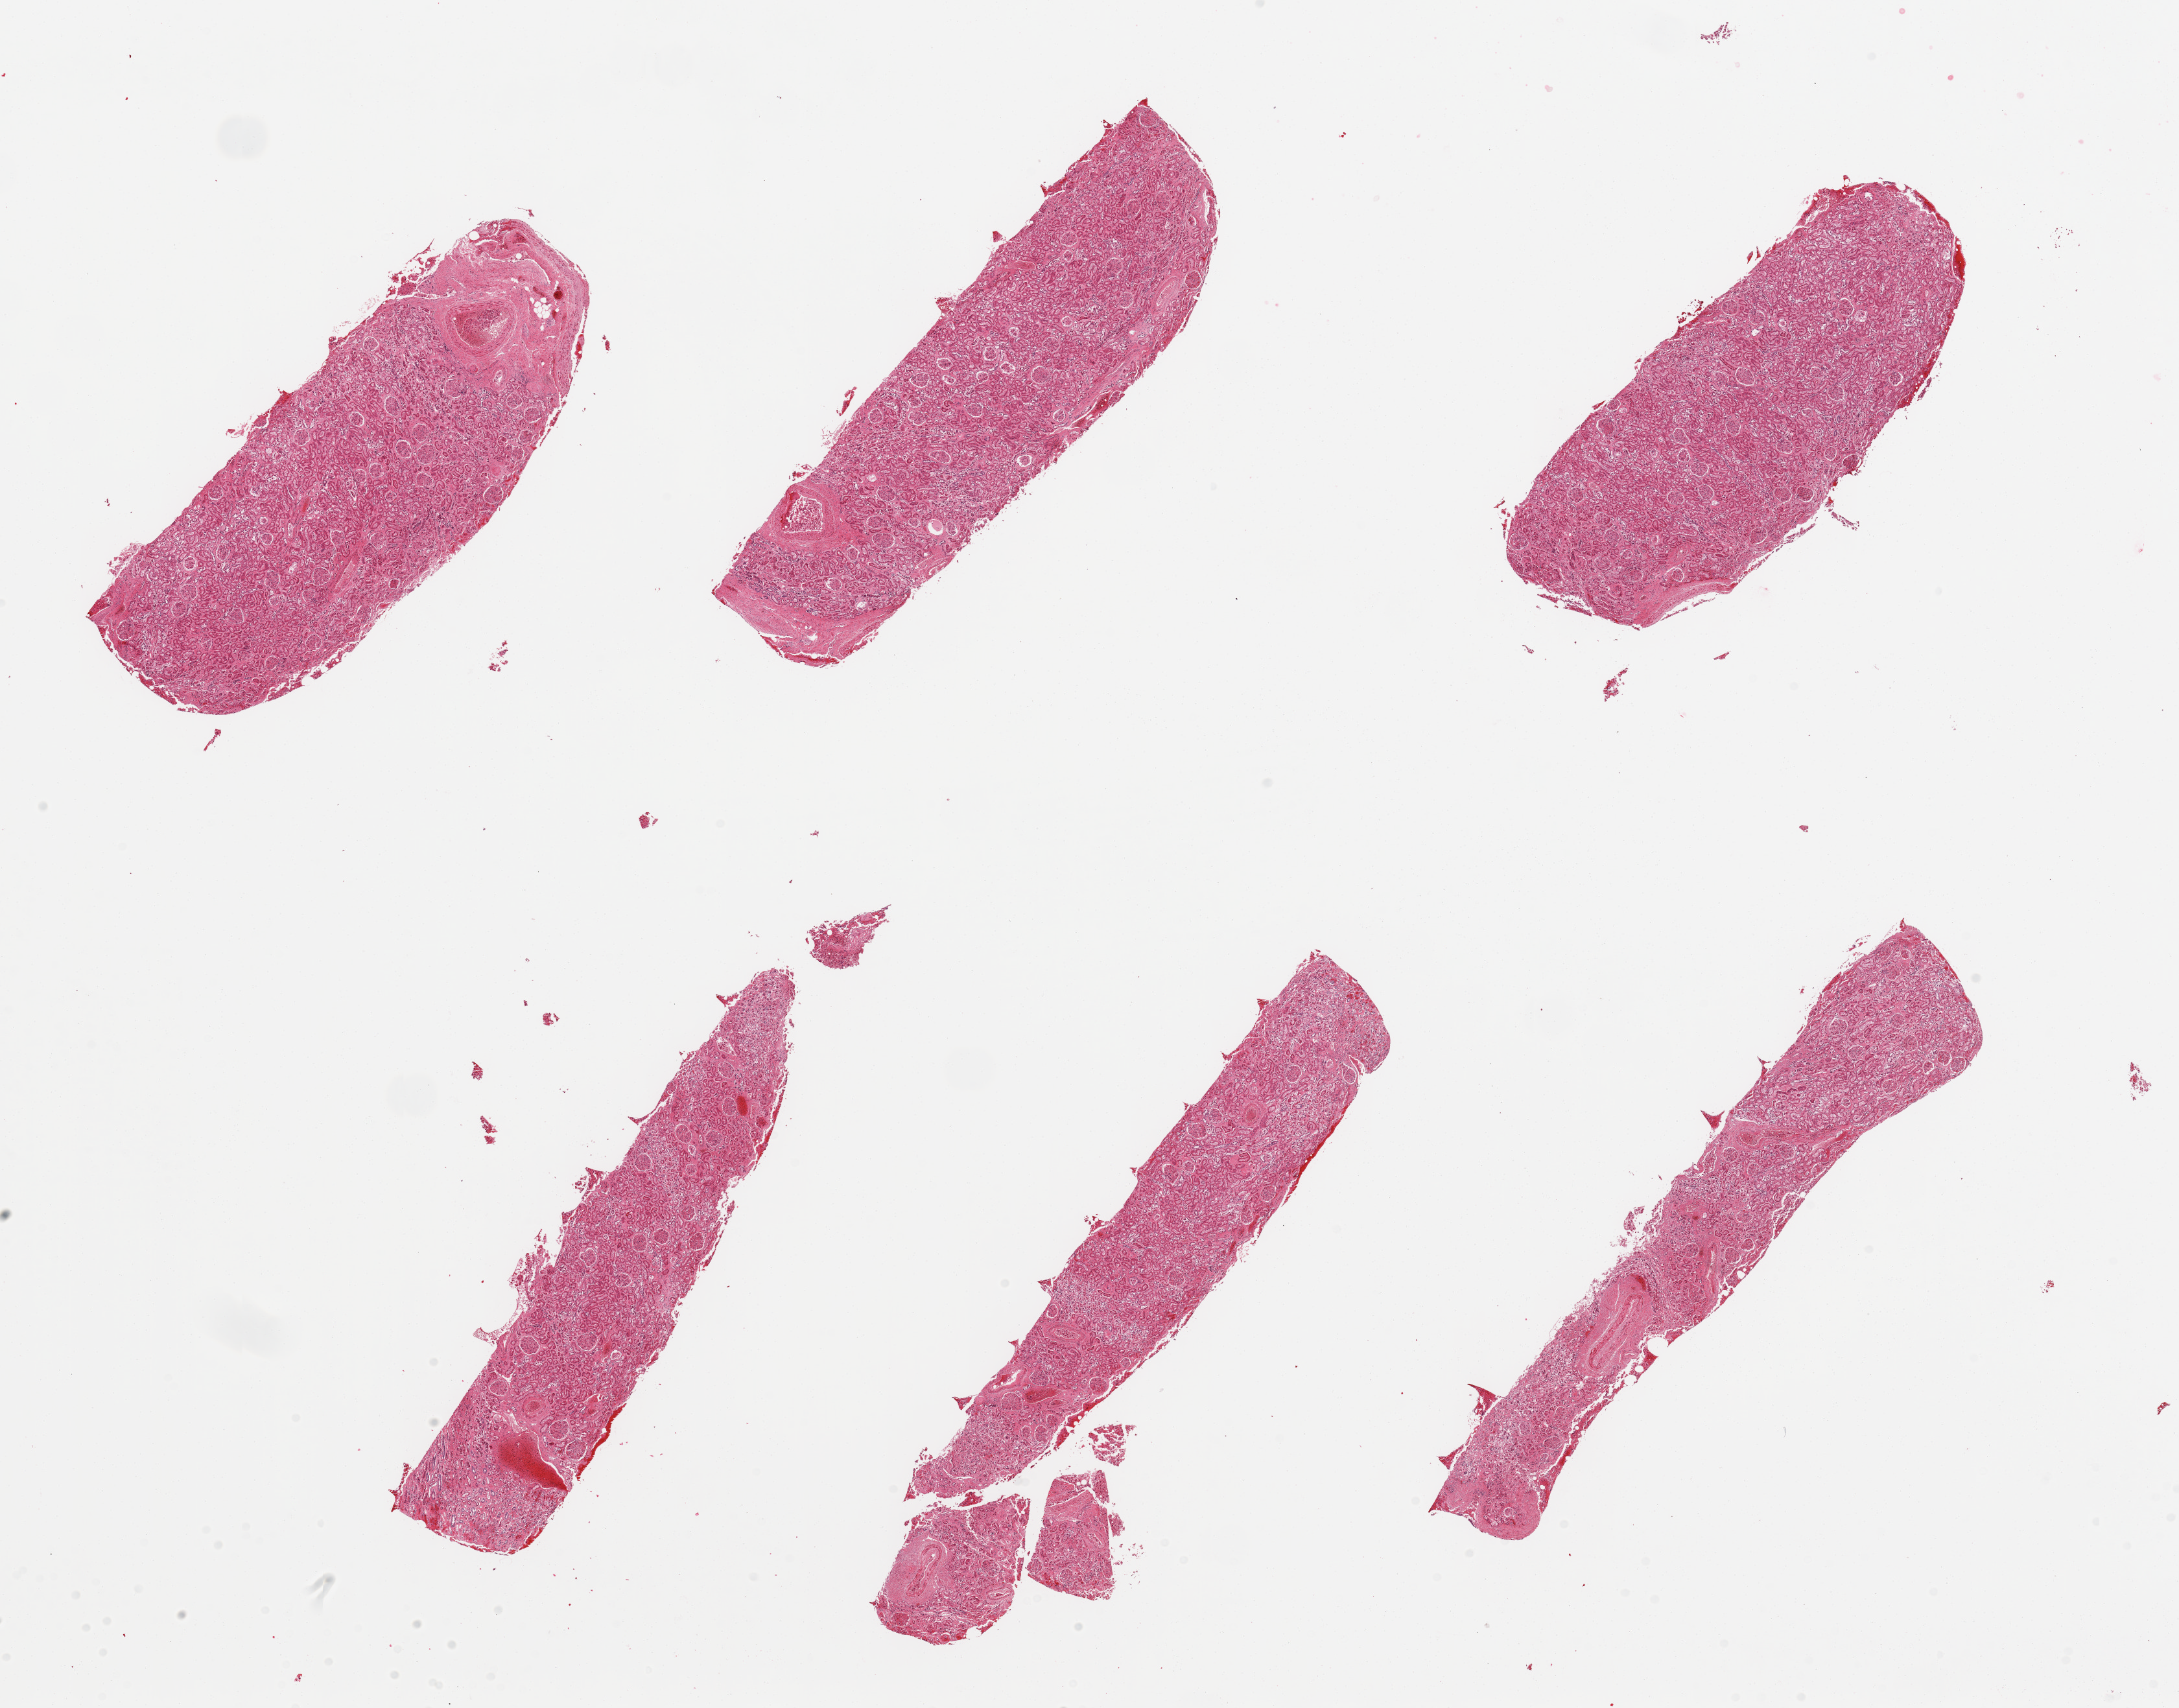
Whole-slide image, hematoxylin and eosin (H&E) stain, brightfield, a low-resolution overview of the entire scanned area, about 26.6 x 20.8 mm. PAXgene-fixed, paraffin-embedded tissue. Sampled site (target tissue): renal cortex. Tissue donor sample. Male donor.
Pathologist's review note for this sample: 6 pieces; no active or chronic lesions.